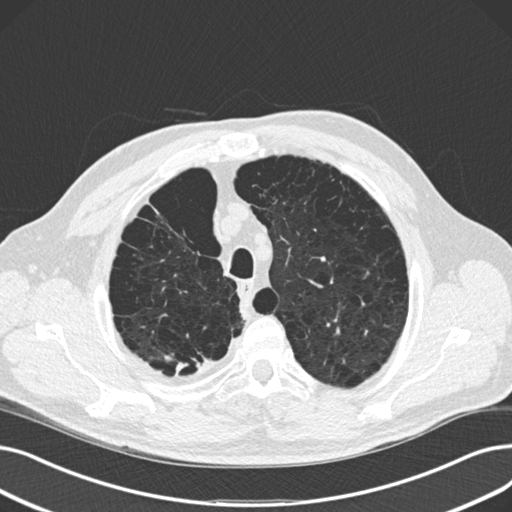
Low-dose screening chest CT, one axial slice; slice 129 of 165 in the series (ordered by position); reconstruction kernel B30f; 120 kVp; lung window (W 1500 / L -600 HU); 2 mm slice thickness; 512 × 512 image matrix, field of view 369 × 369 mm.
Structures marked on this image (manually delineated by an expert):
- lesion 2 (tumor, upper lobe of right lung): bounding box (x1, y1, x2, y2) in pixels: (175, 362, 188, 373)